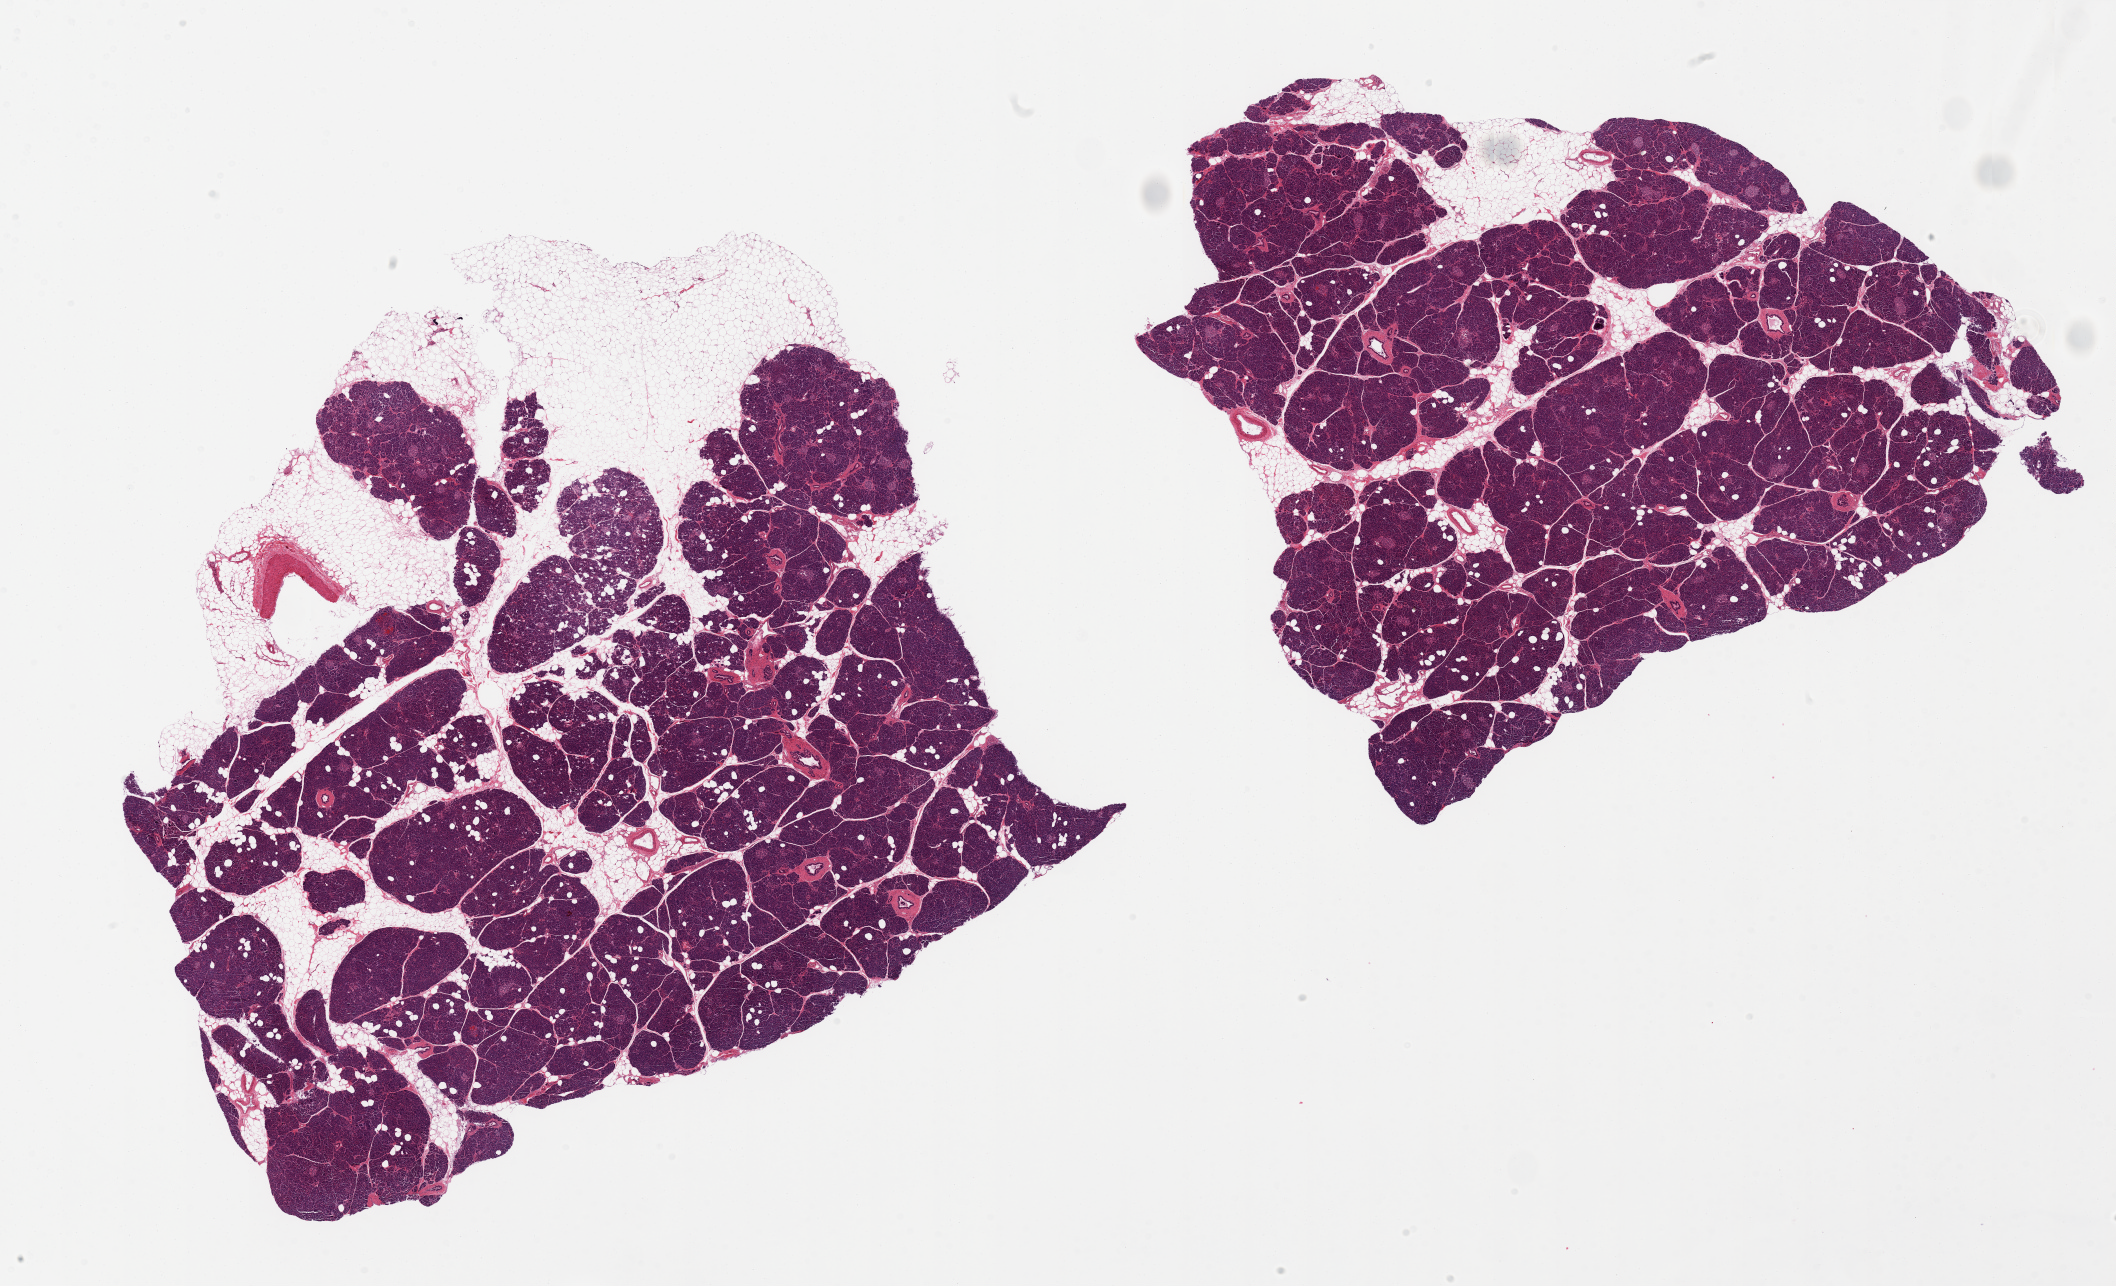
Digitized hematoxylin and eosin (H&E)-stained section, brightfield, a low-resolution overview of the entire scanned area, about 33.5 x 20.3 mm, PAXgene-fixed paraffin-embedded (PFPE) section, target tissue: pancreas, donor tissue sample.
Review note (as recorded): 2 pieces, include 20 and 40% fat (attached and internal).